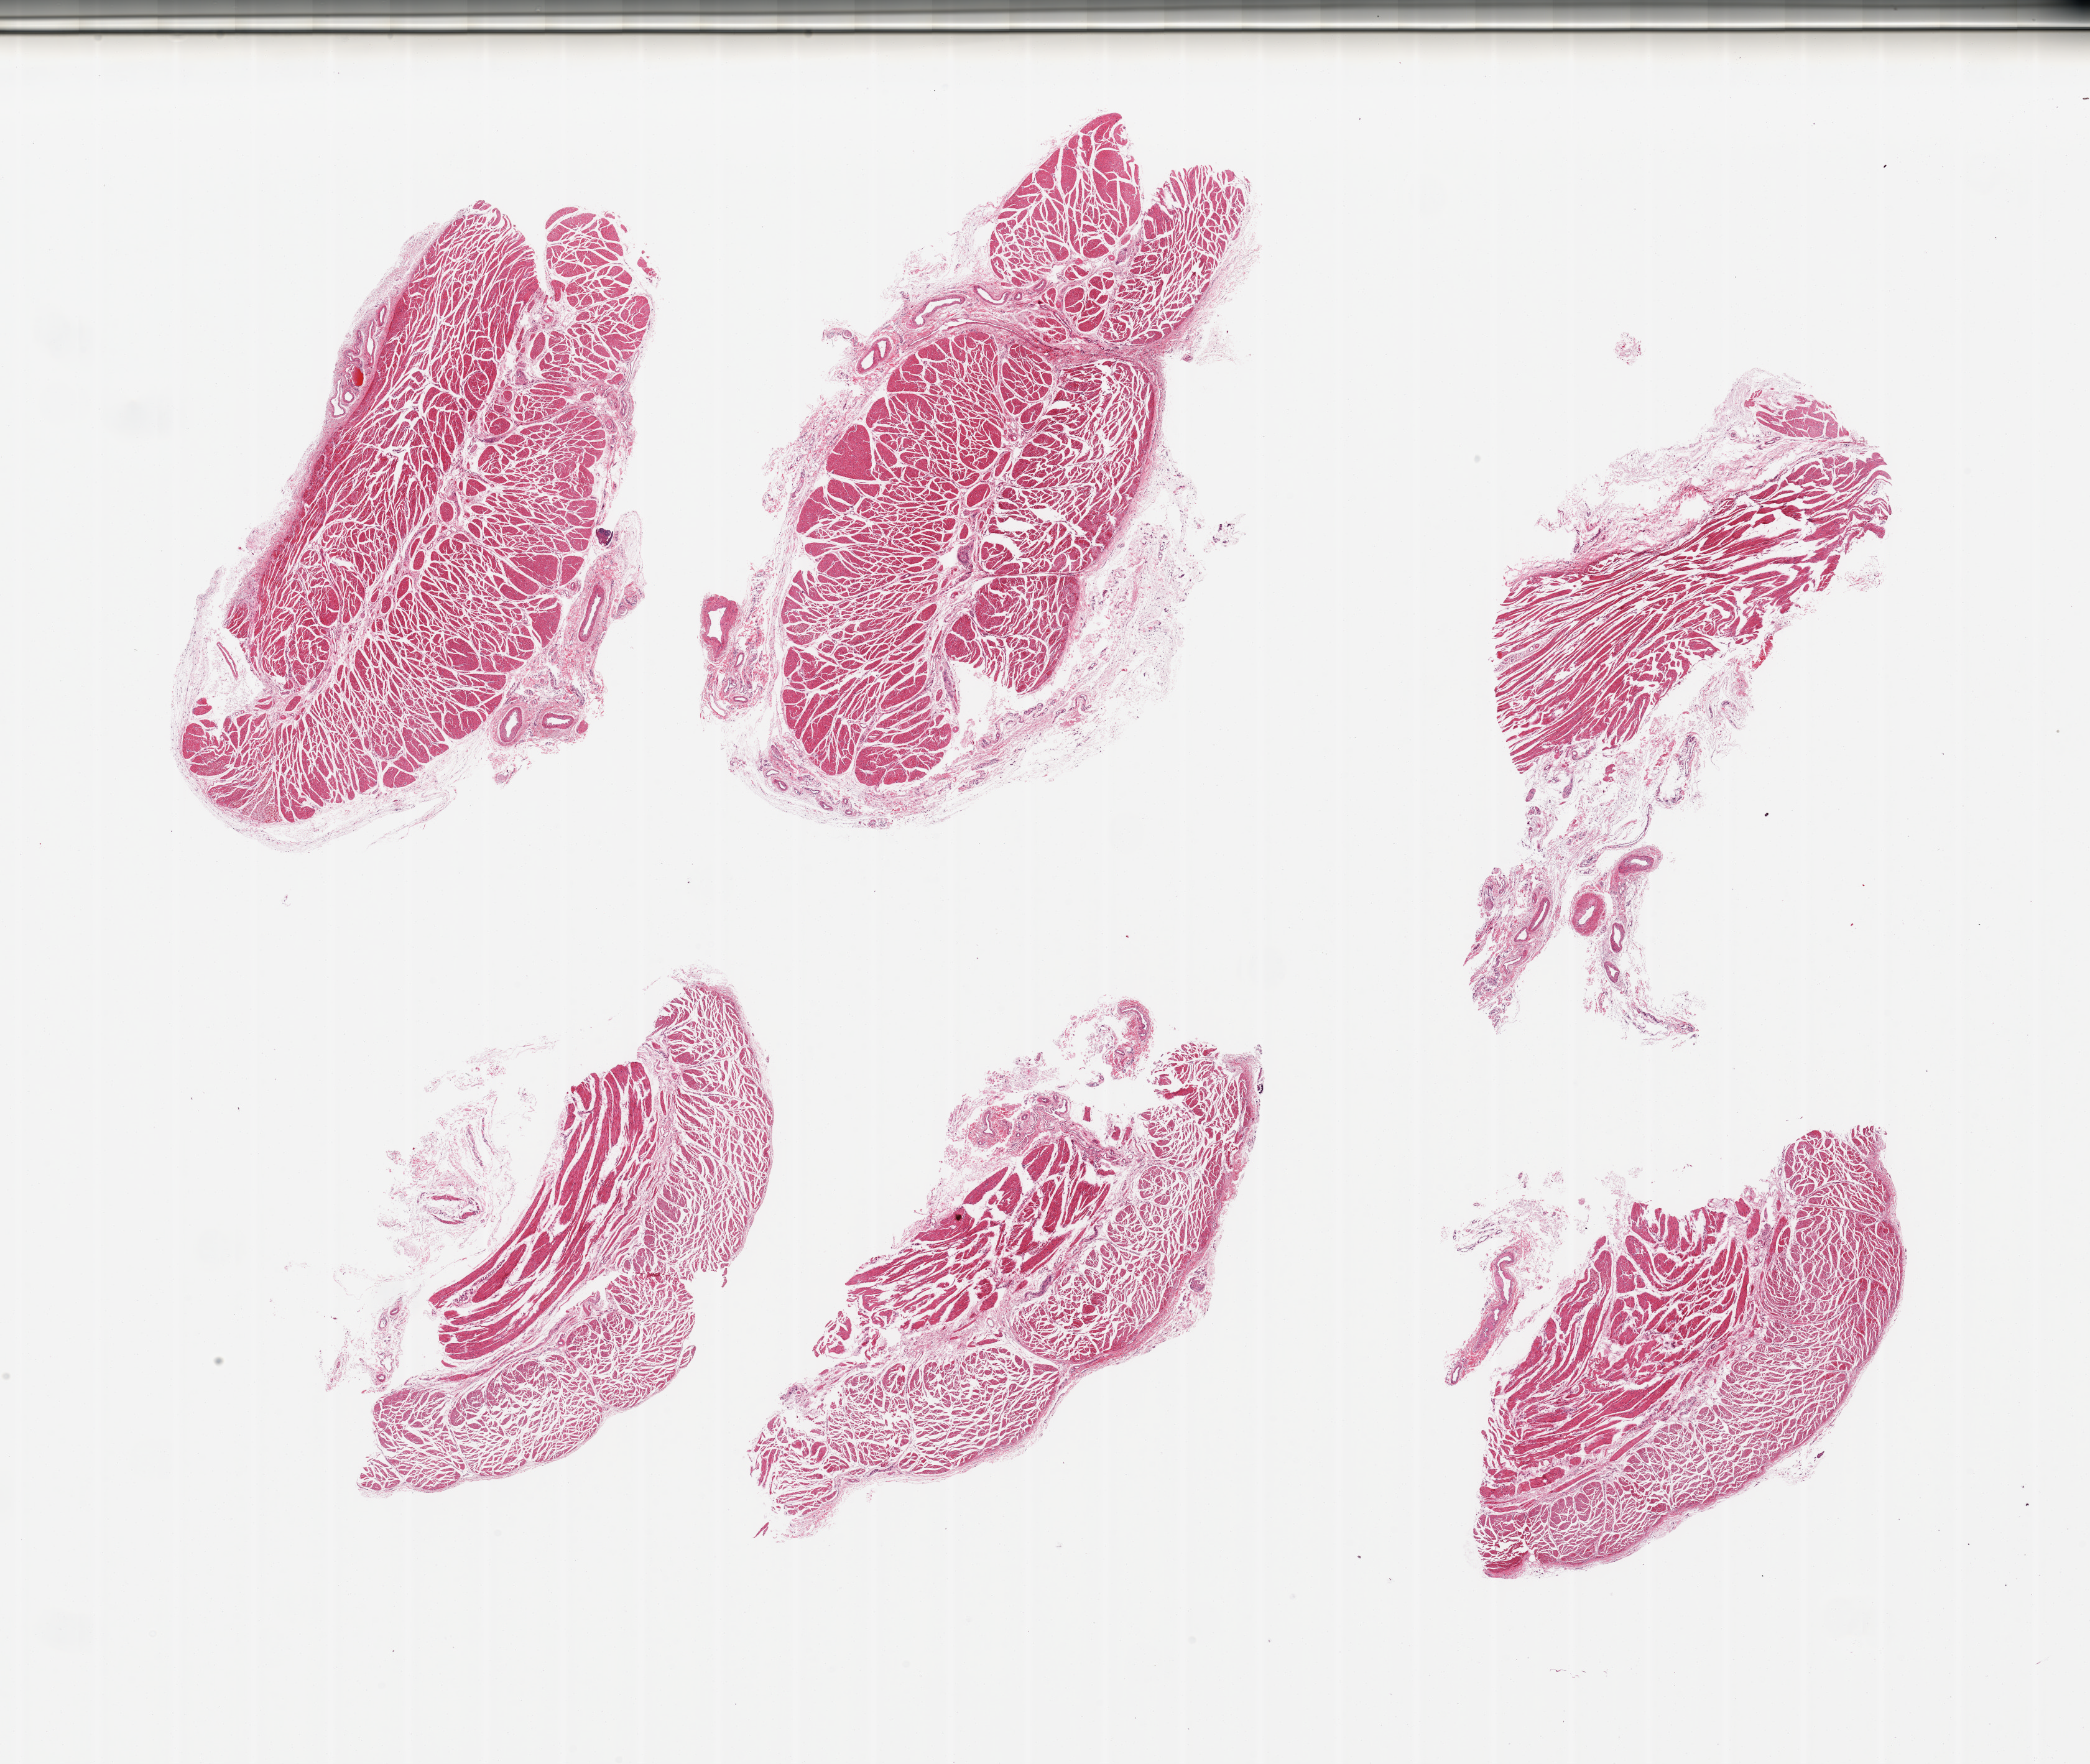
Whole-slide image, haematoxylin and eosin stain — shown as a low-resolution overview of the whole scanned area (about 26.6 x 22.4 mm). PAXgene-fixed, paraffin-embedded tissue. Target tissue: esophageal muscle. Donor tissue sample. Donor sex: female.
• pathologist's review note for this sample: 6 pieces; muscle with small amount of submucosa